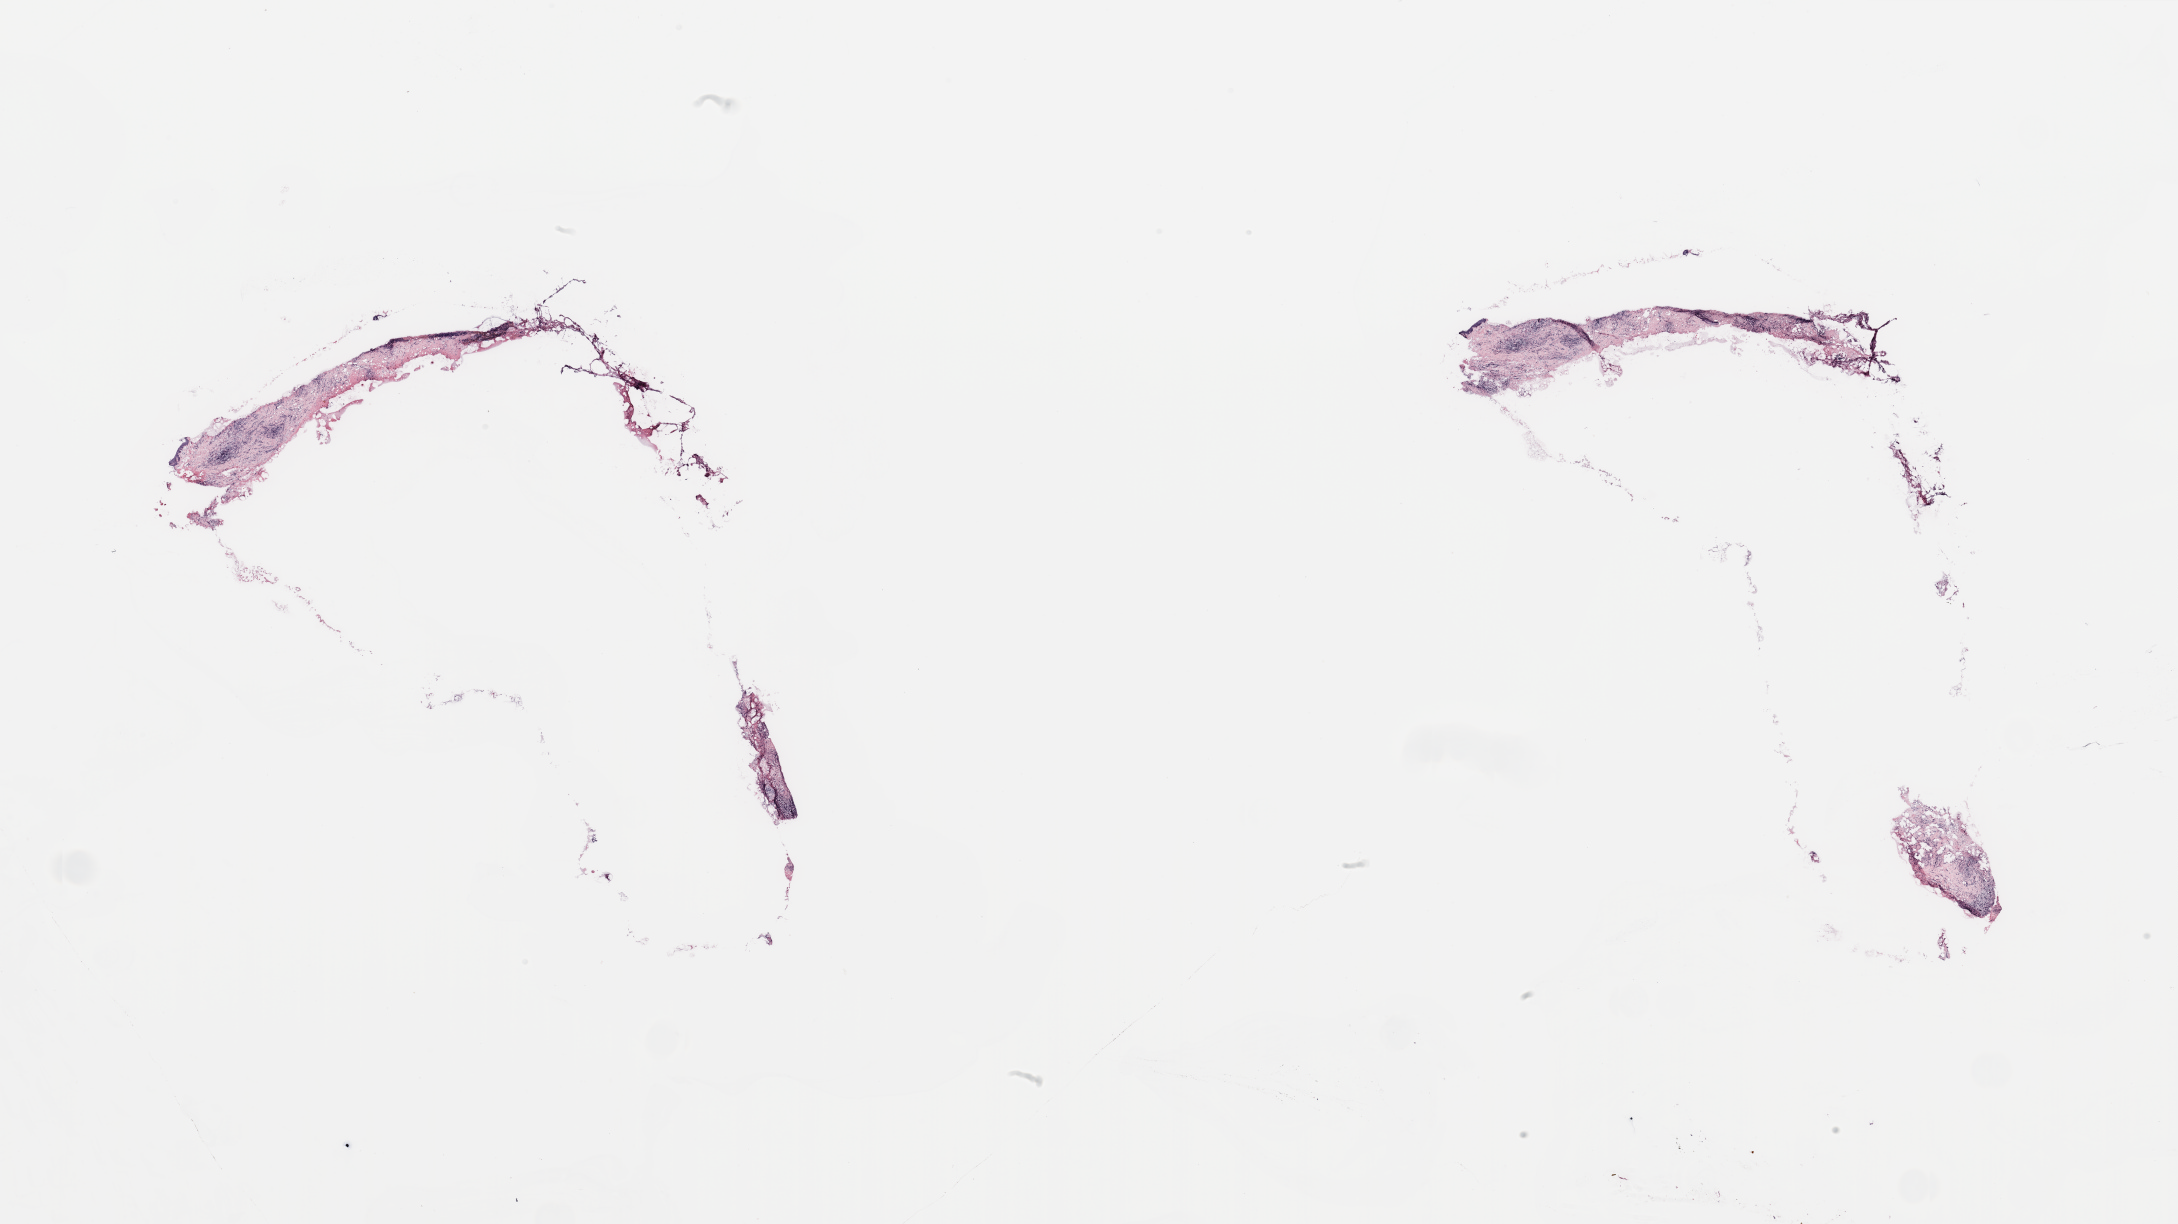
Whole-slide histology image, Hematoxylin and eosin (H&E) stained, low-resolution overview of the scanned area, about 34.5 x 19.4 mm (acquisition: 20x scan). Breast, tissue type not recorded.
Patient diagnosis (cohort enrolment): breast cancer (breast).